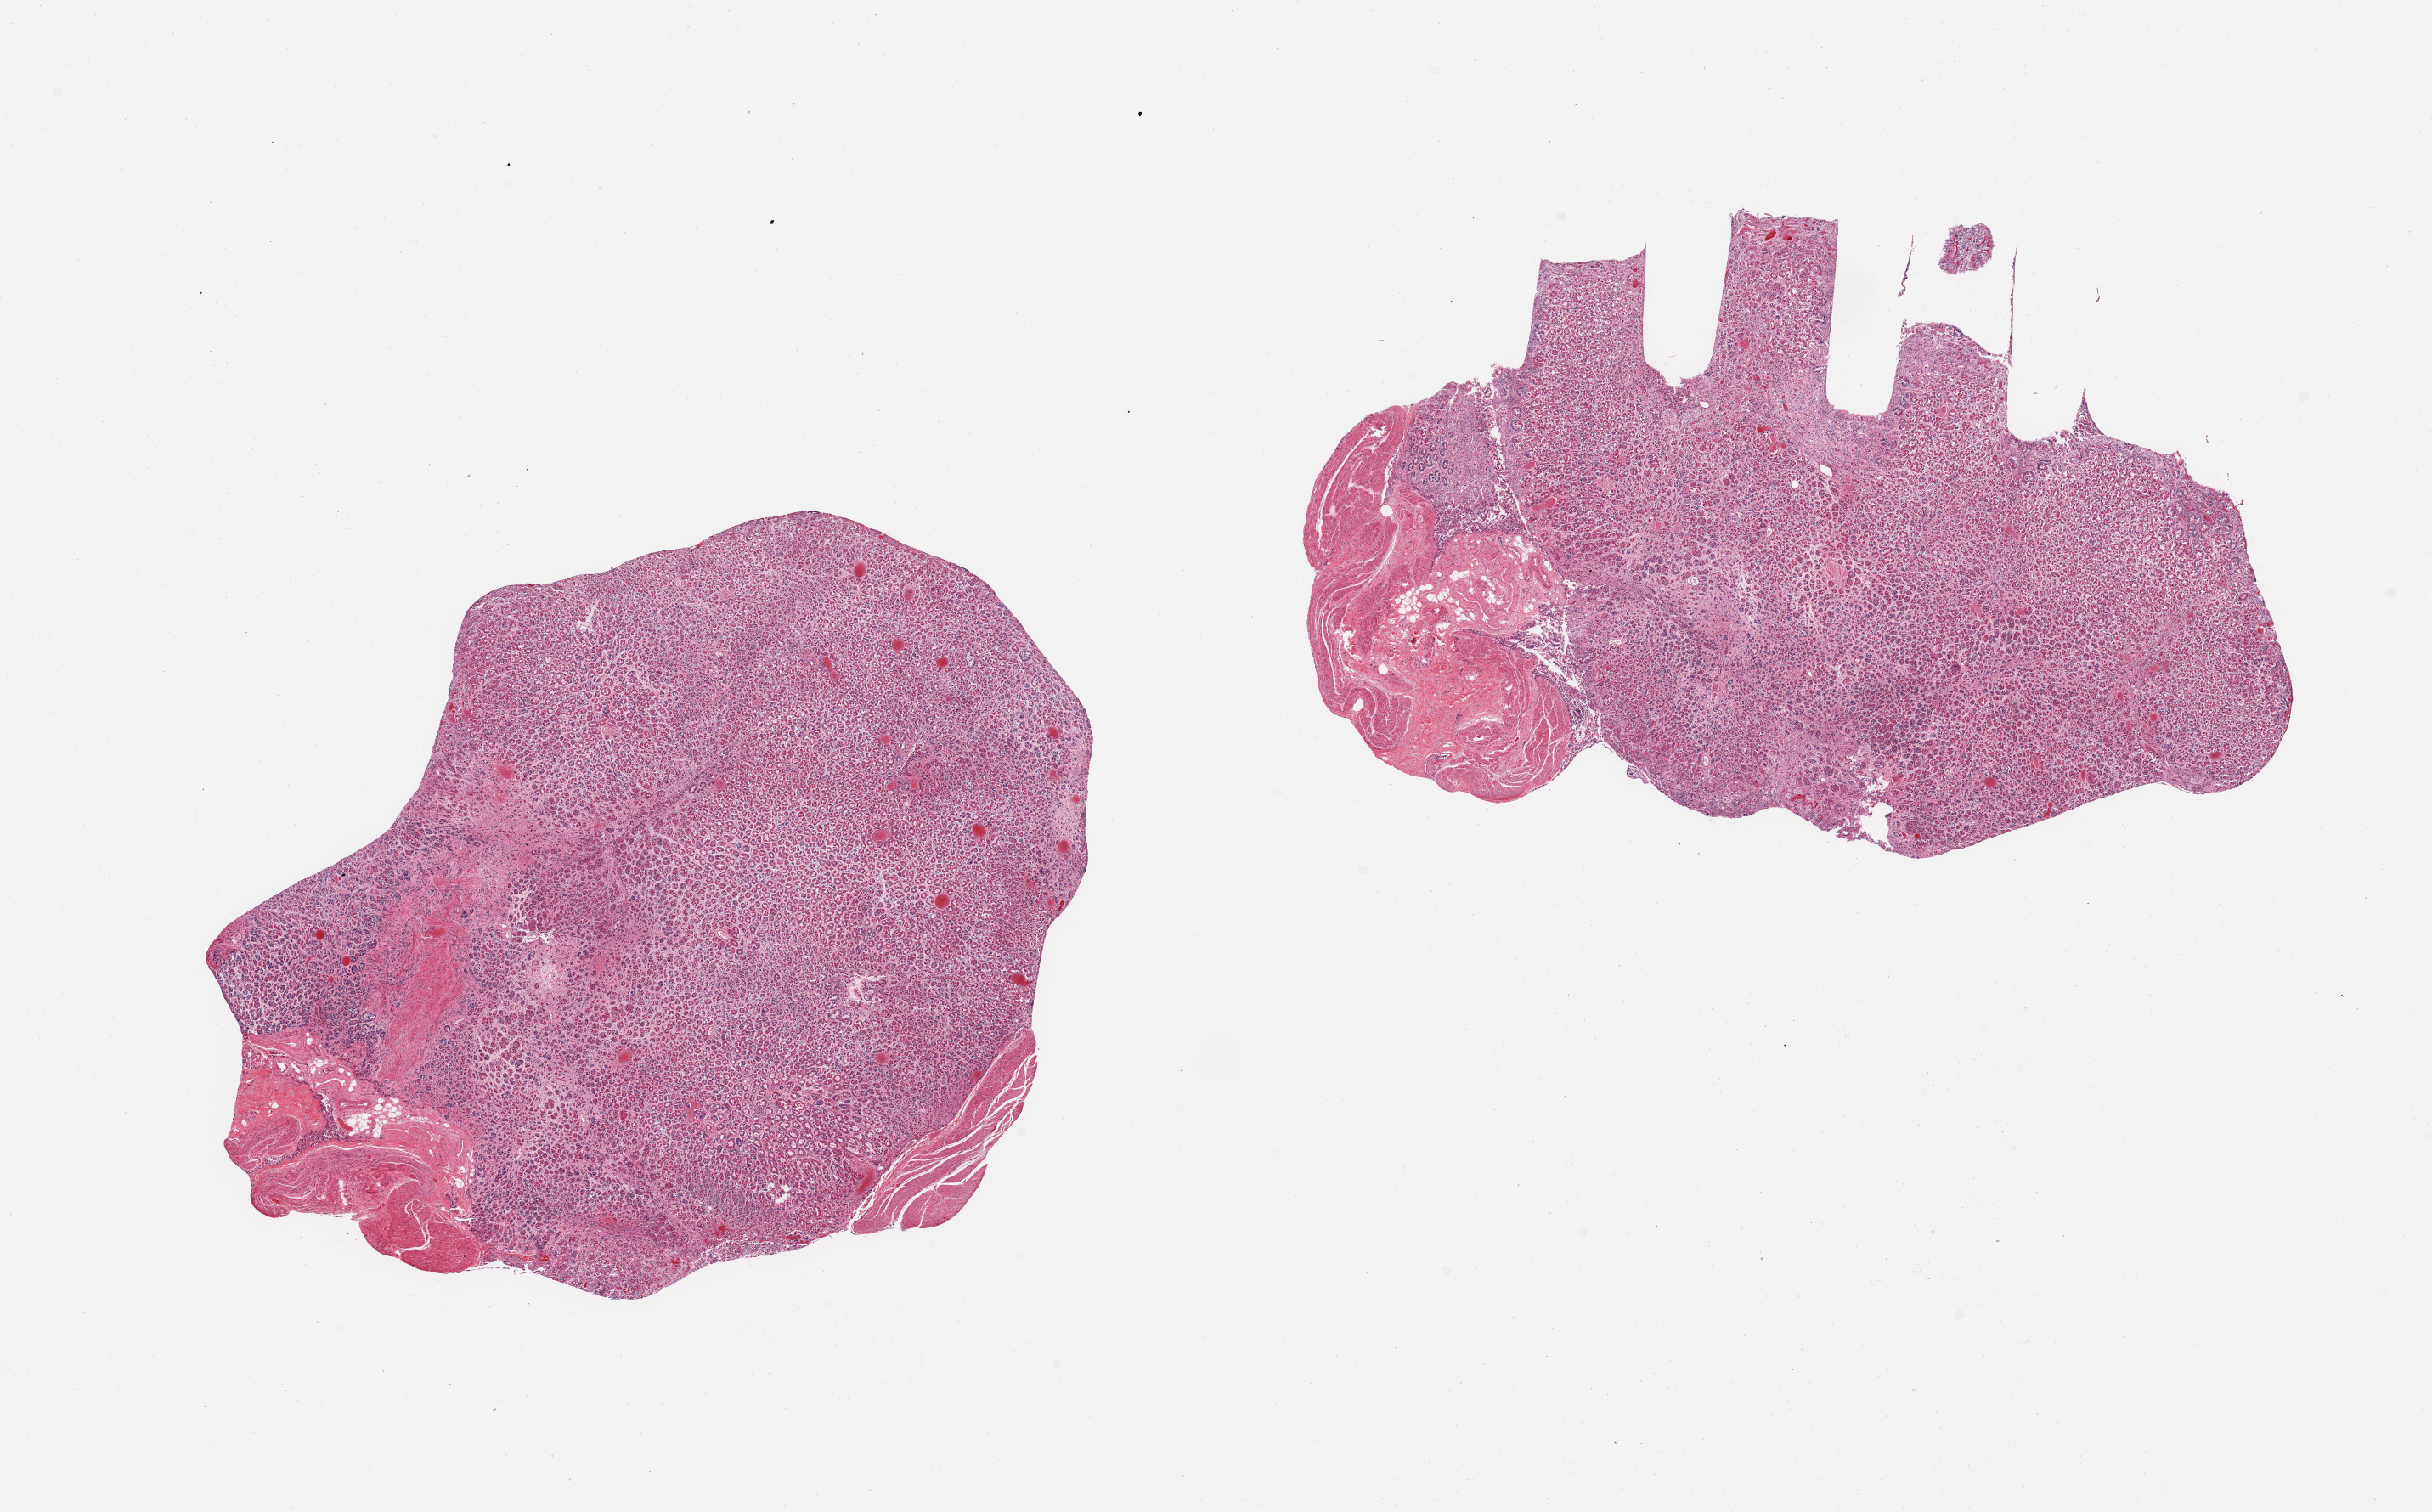
Hematoxylin and eosin (H&E) whole-slide image, brightfield, low-resolution overview of the scanned area, about 22.6 x 14.1 mm, PAXgene-fixed paraffin-embedded (PFPE) section, target tissue: stomach, tissue donor sample. Donor: male.
Pathologist's review note for this sample: 2 pieces, embedded en face sp thickness not evaluable. Autolysis moderately advanced in mucosa.